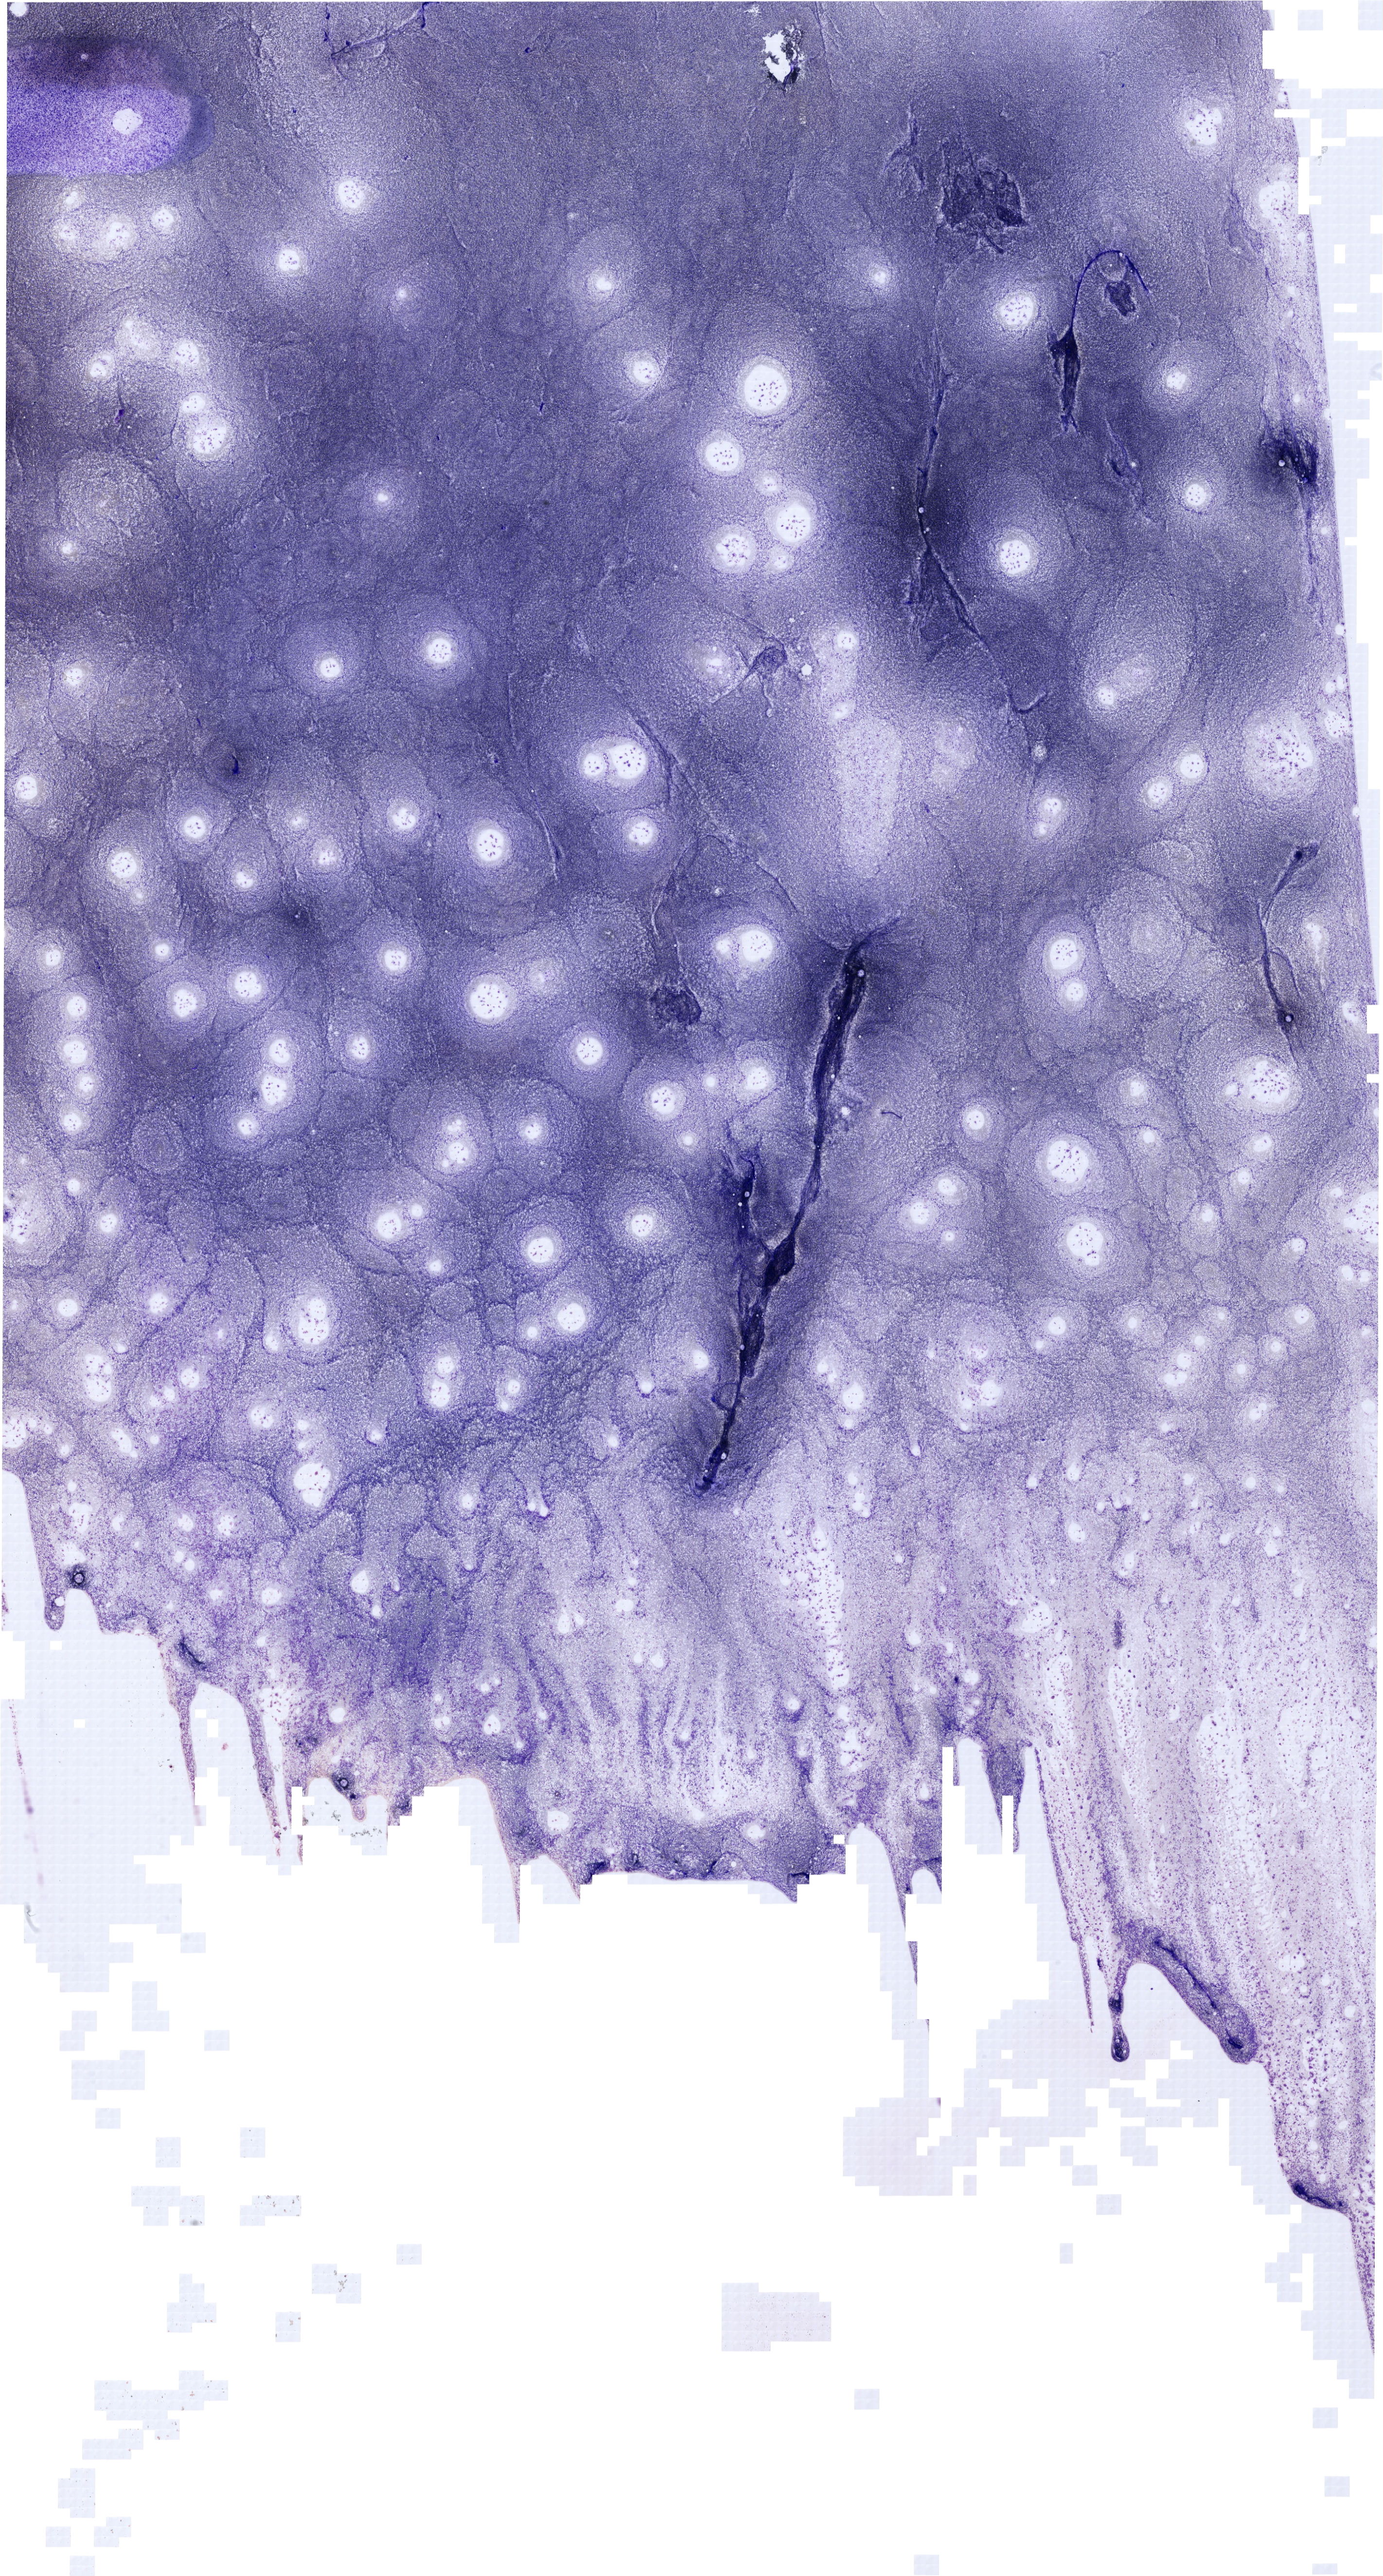
Whole-slide image of a May-Grünwald-Giemsa (MGG)-stained bone marrow aspirate smear, whole scanned area (about 22.2 x 41.4 mm) shown as a low-resolution overview. Female patient.
• diagnosis: T Acute Lymphoblastic Leukemia